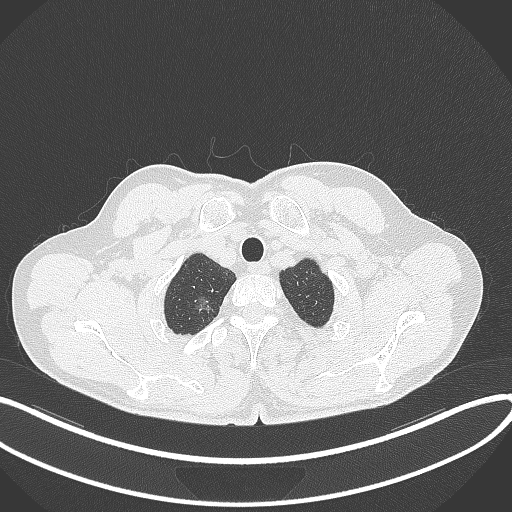
Chest CT, one axial slice; position 354 of 407 along the scan axis; reconstruction kernel B70f; lung window (W 1500 / L -600 HU); 512 × 512 image matrix, field of view 400 × 400 mm. Male patient, age 58 years. From the clinical record (not read from this slice): clinical TNM (as recorded): T1c N0 M0; histopathological grade: G1-2.
Outlined on this slice (bounding box drawn by a radiologist):
- lung tumour (recorded histology: adenocarcinoma): box from (x=188, y=295) to (x=217, y=318) px